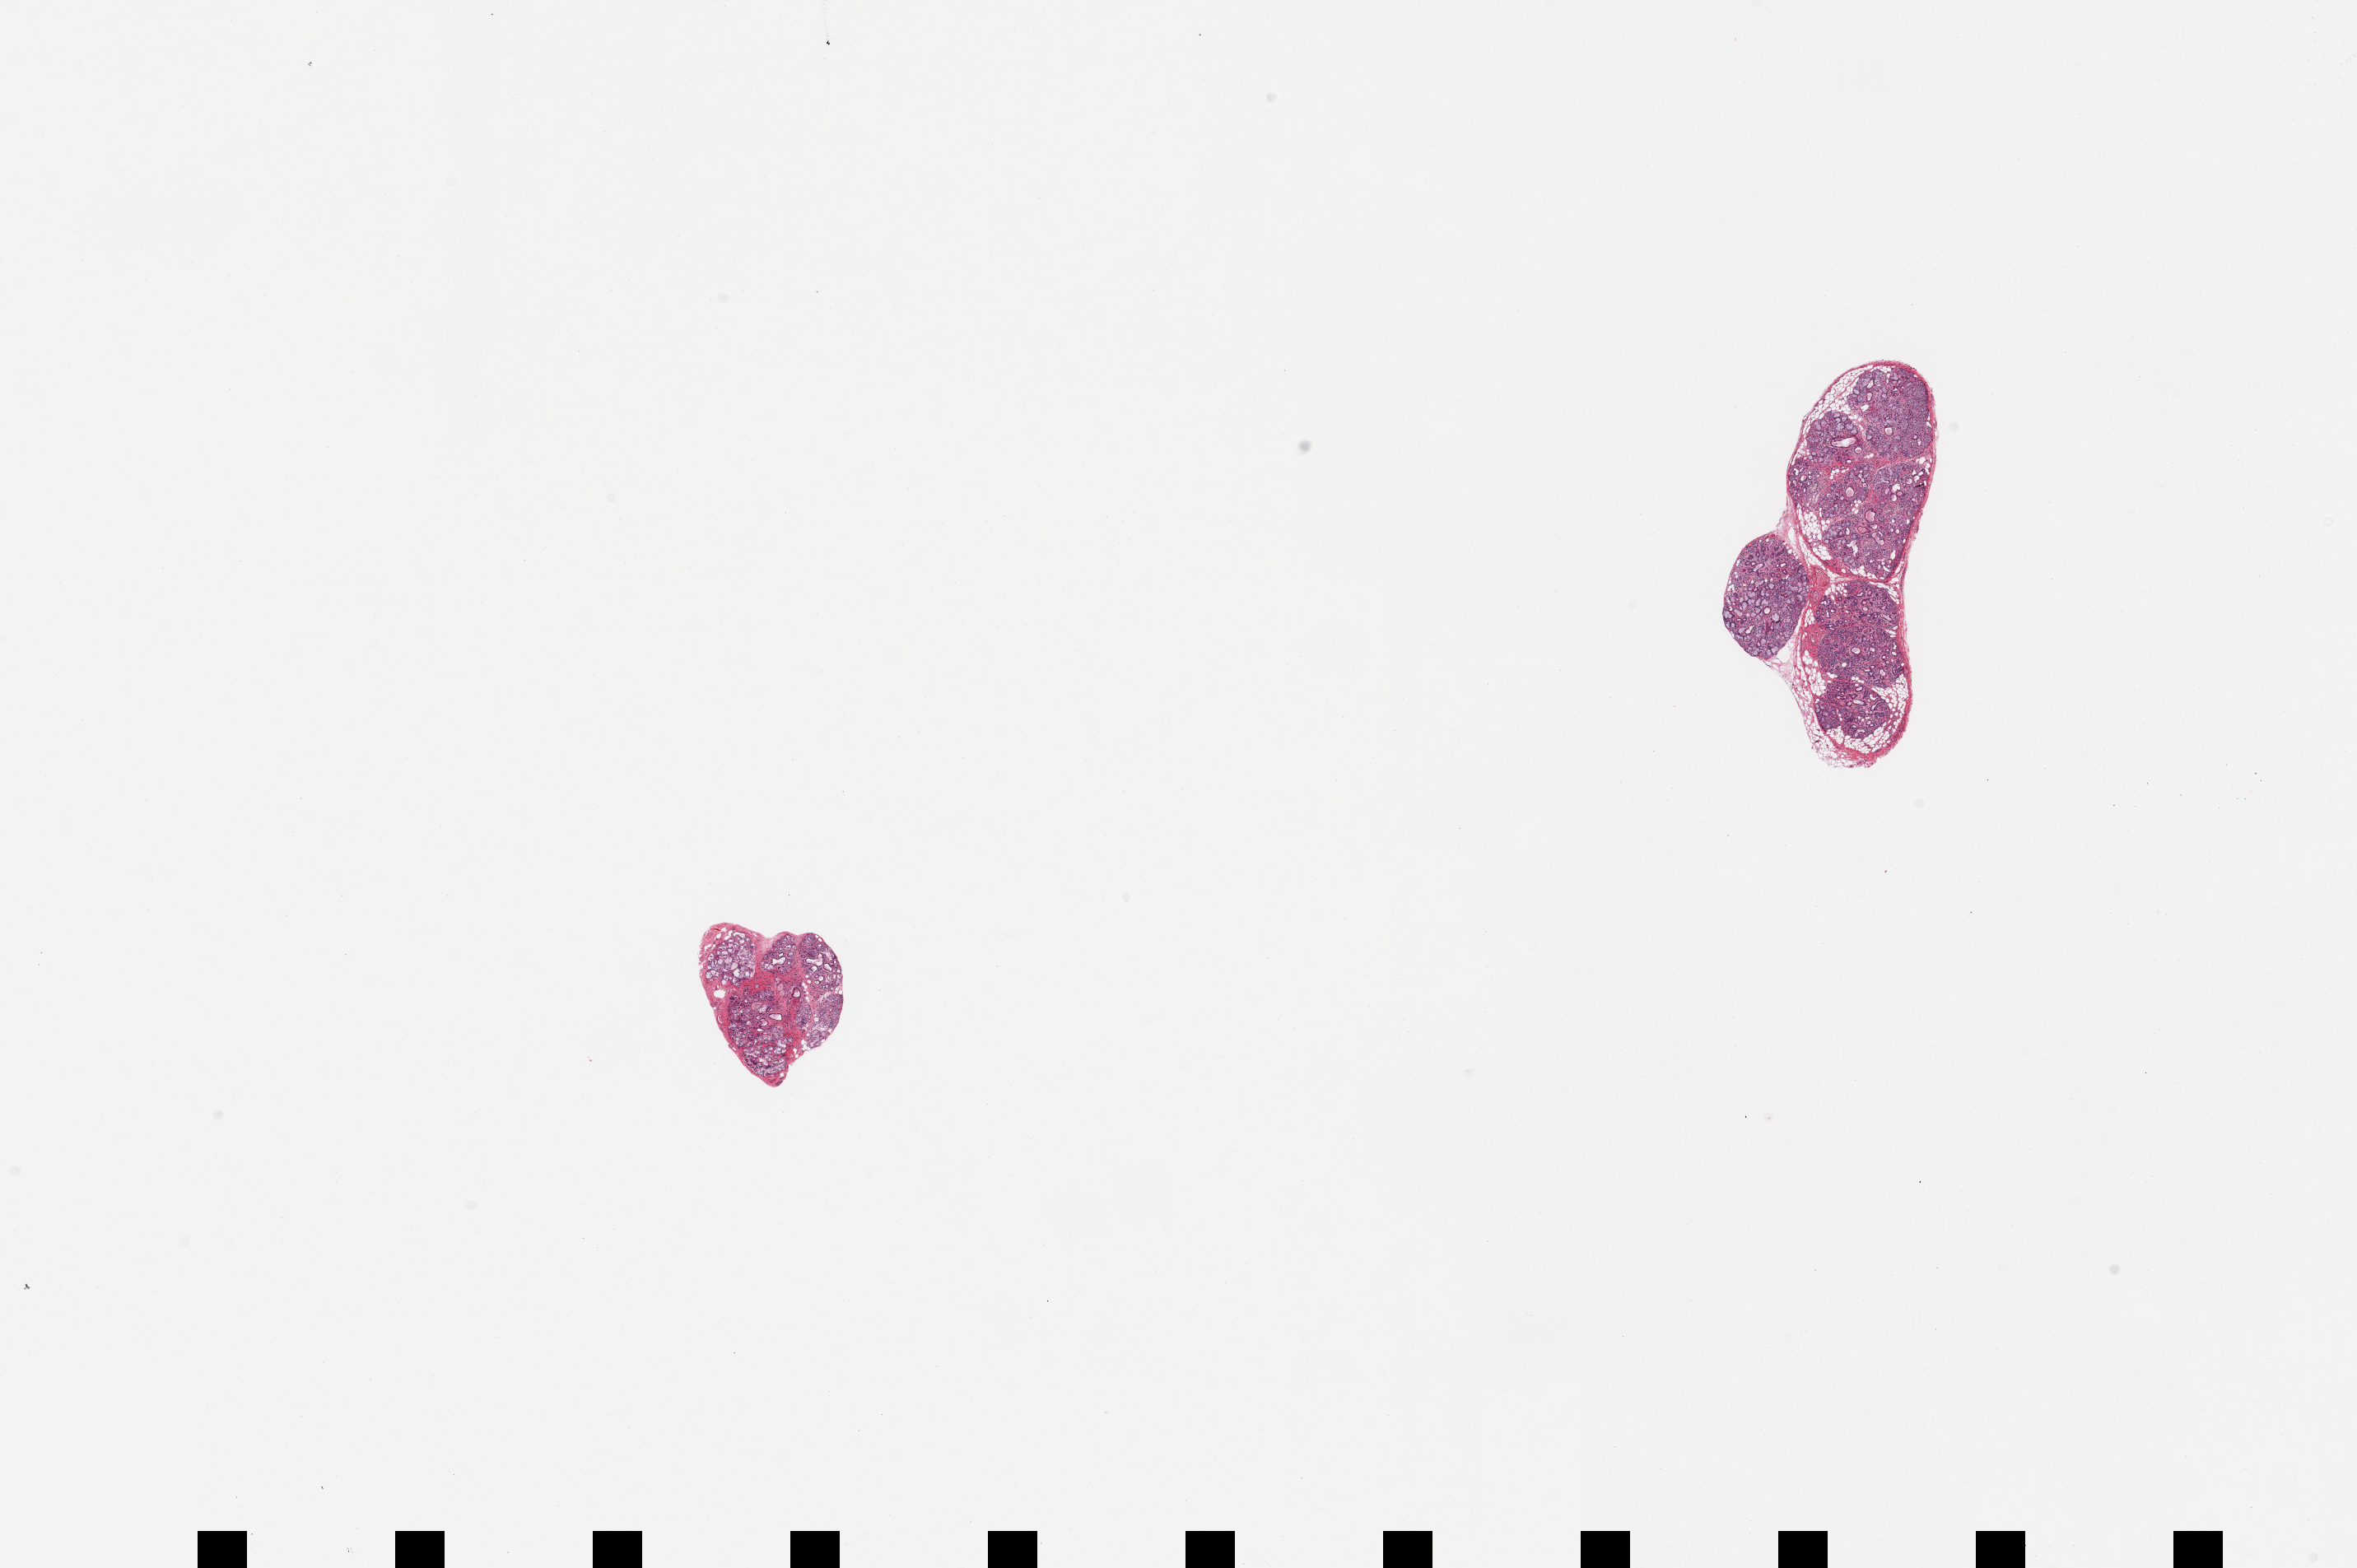
Digitized haematoxylin and eosin-stained section, whole scanned area (about 22.6 x 15.1 mm) shown as a low-resolution overview, PAXgene-fixed paraffin-embedded (PFPE) section, target tissue: minor salivary gland, donor tissue sample.
- review note (as recorded): 2 pieces; well trimmed, many plasma cells